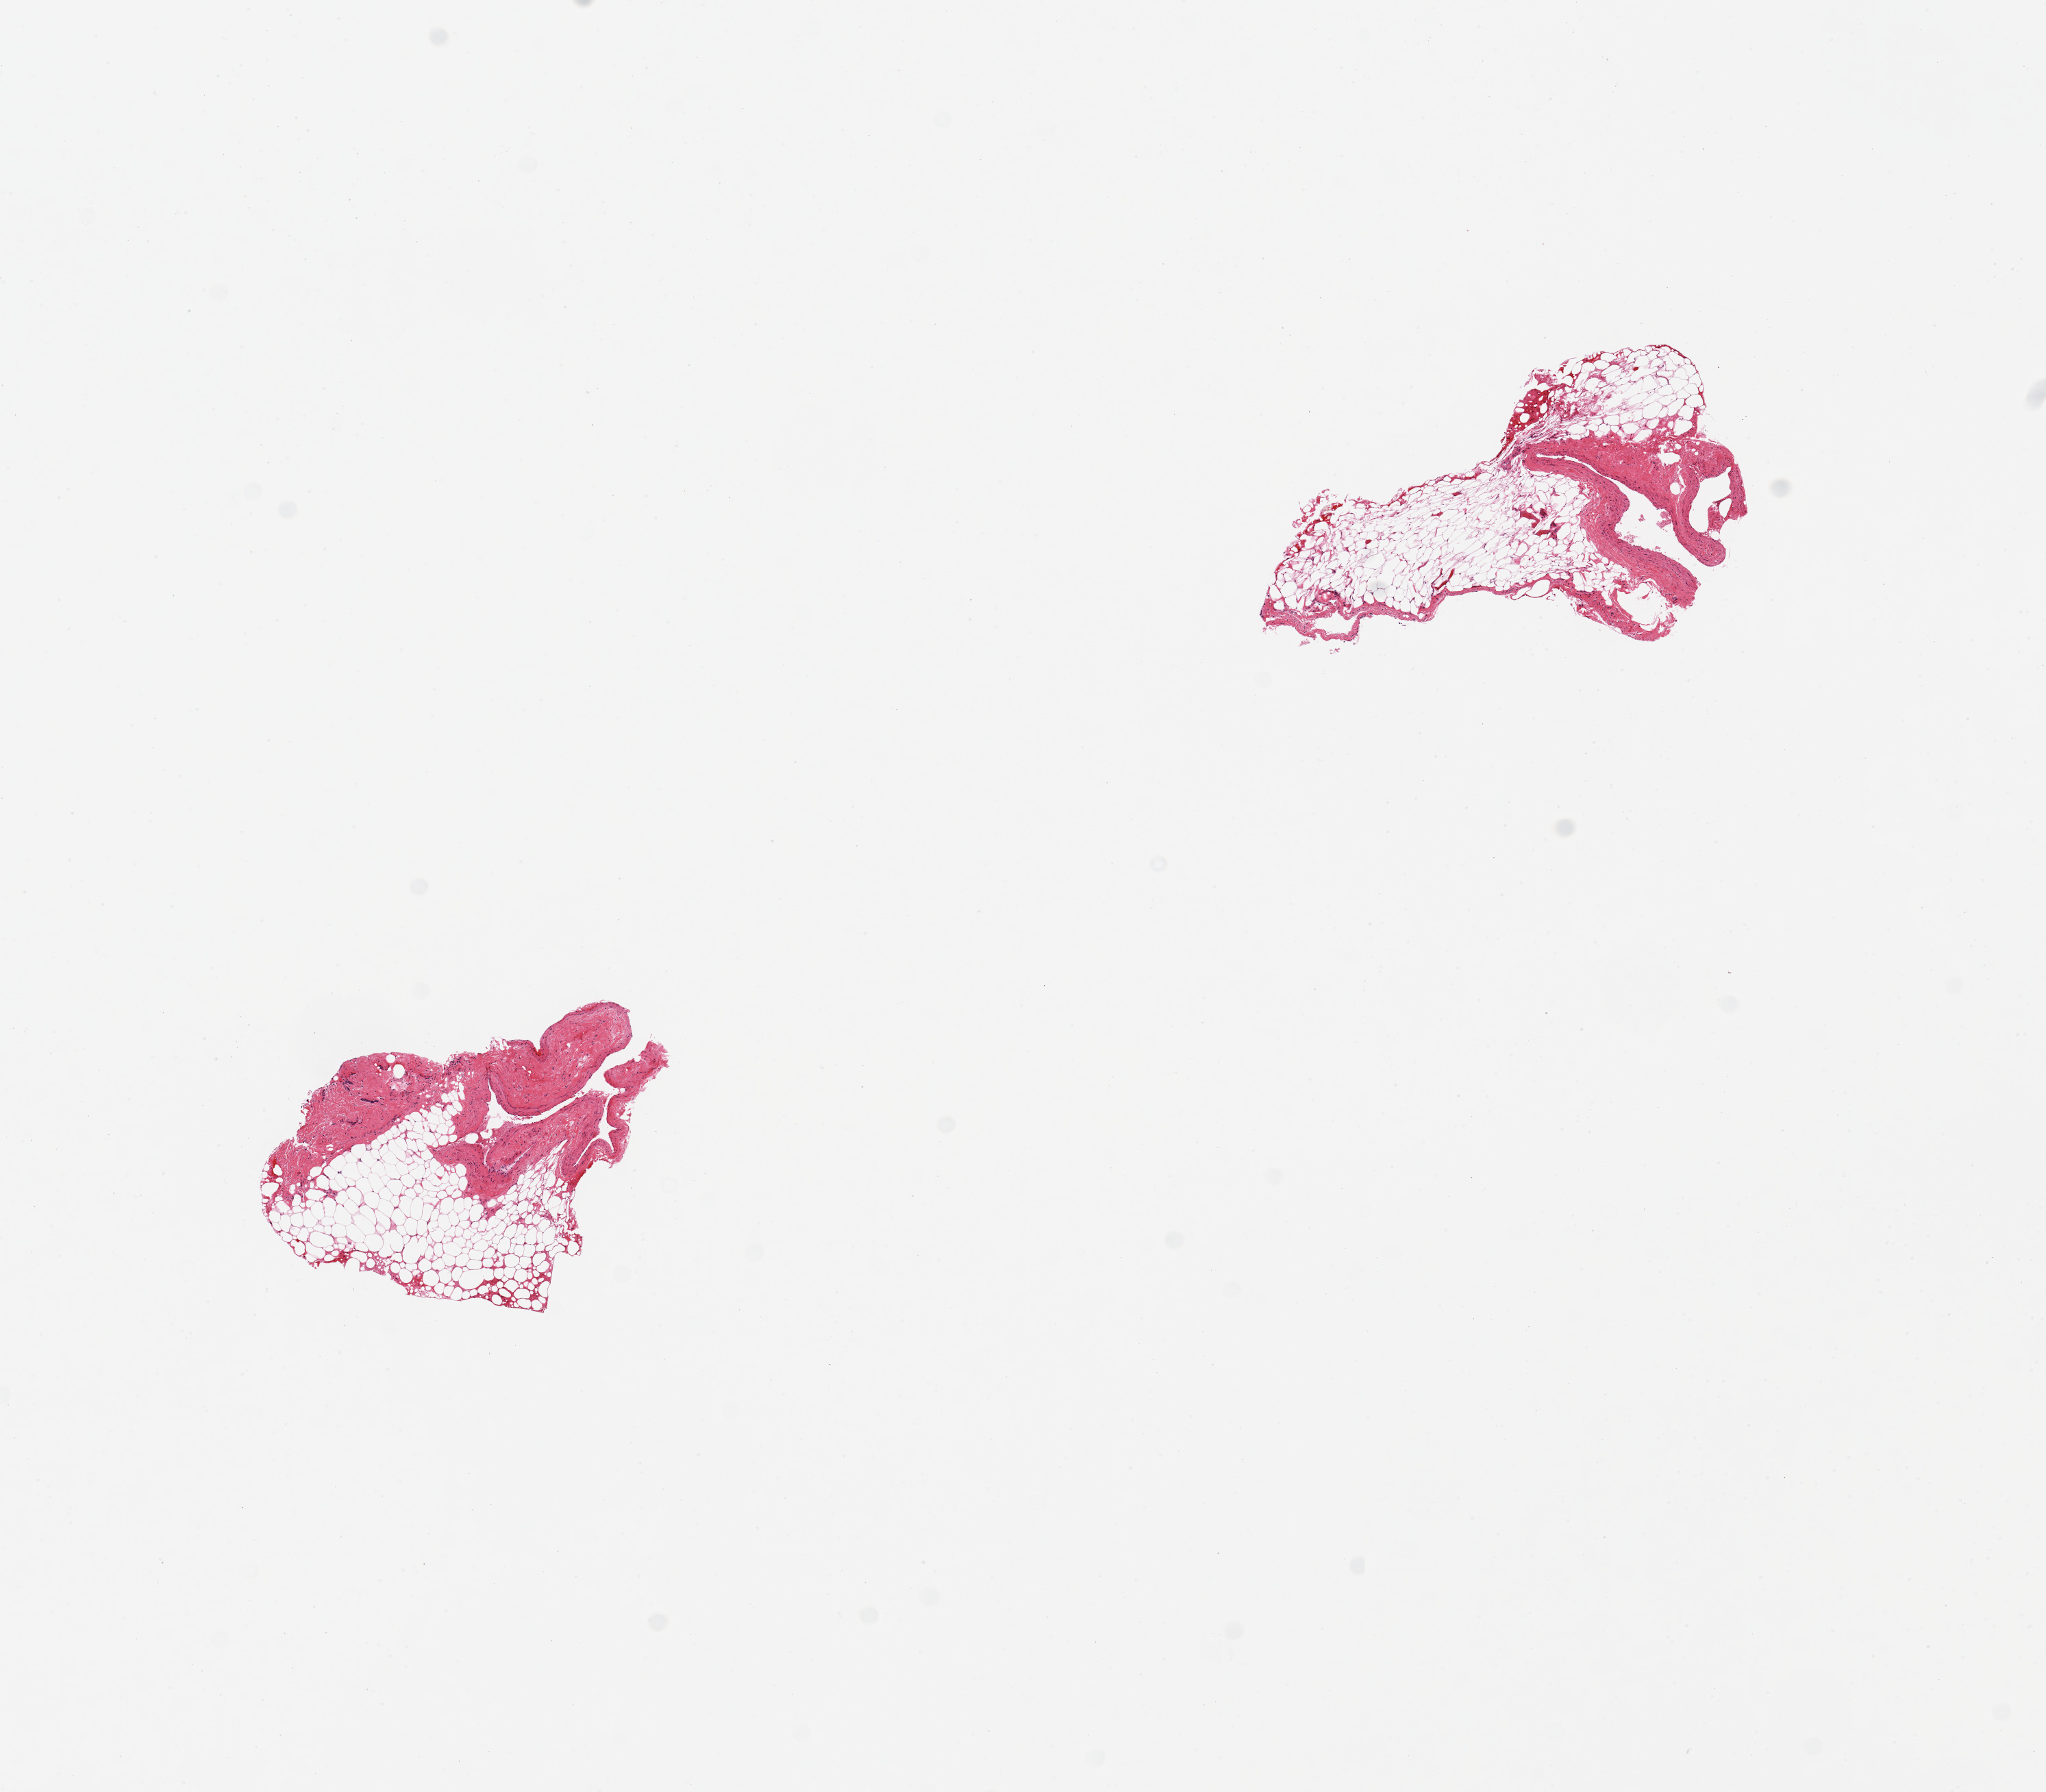
Whole-slide image, hematoxylin and eosin (H&E) stain, brightfield — a low-resolution overview of the entire scanned area, about 11.8 x 10.3 mm (acquisition: 20x scan); PAXgene-fixed paraffin-embedded (PFPE) section; sampled site (target tissue): coronary artery; tissue donor sample. Donor sex: male.
• review note (as recorded): 2 pieces, small vessels, no atherosis; prominent adherent fat up to ~1.5mm